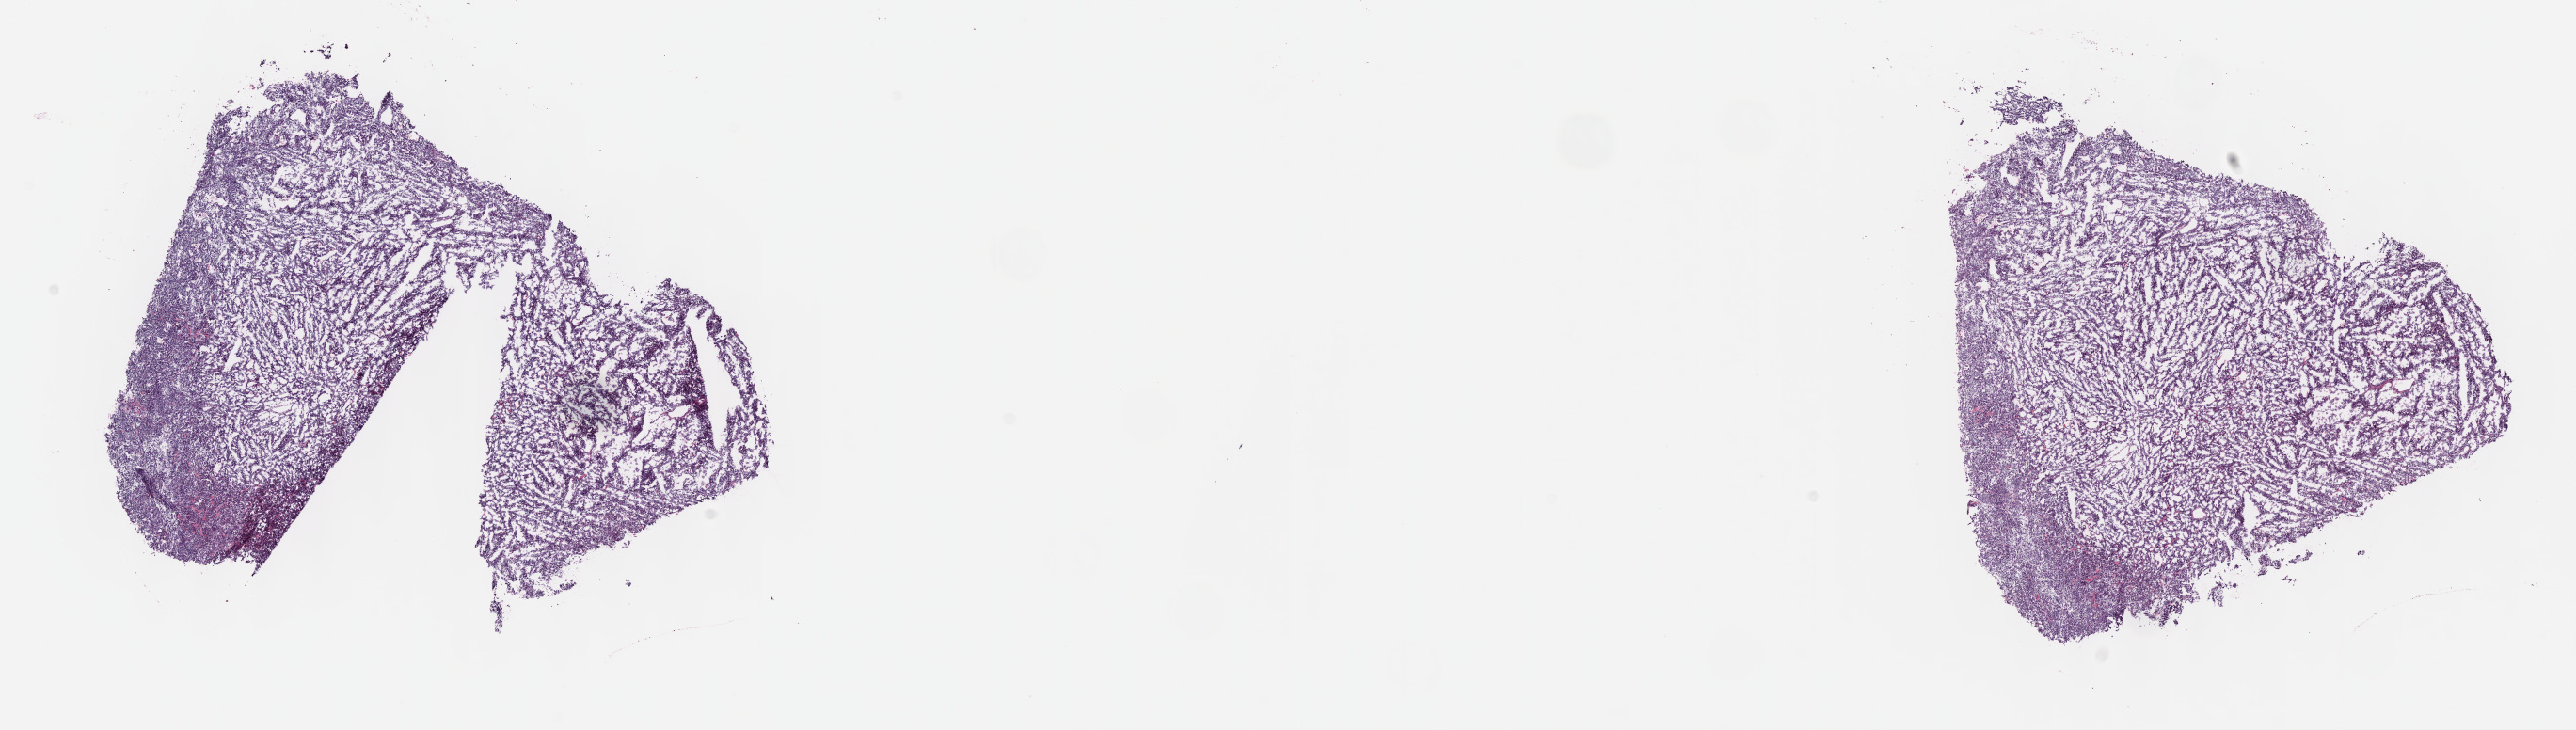
Whole-slide histology image, Hematoxylin and eosin (H&E) stained — shown as a low-resolution overview of the whole scanned area (about 22.1 x 6.3 mm); frozen section; connective, subcutaneous and other soft tissues, primary tumour sample. Female patient; age at initial diagnosis 20 years. Composition of this section per pathologist review: tumour cells 100%, tumour nuclei 80%, normal cells 0%, stromal cells 0%, necrosis 0%. Infiltration values recorded for this section: lymphocyte infiltration 1%, monocyte infiltration 0%, neutrophil infiltration 0%.
* diagnosis: Synovial sarcoma, biphasic (connective, subcutaneous and other soft tissues of trunk, NOS)